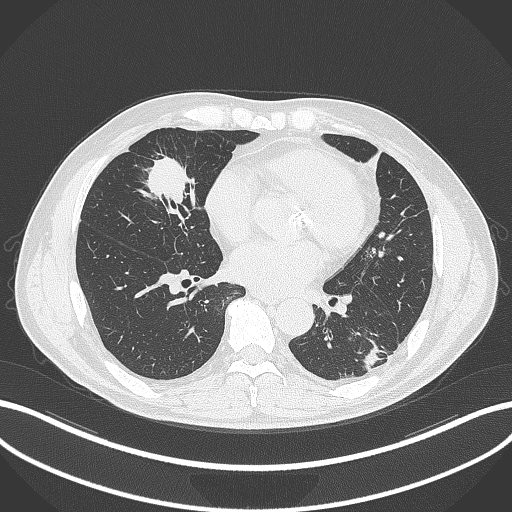
Chest CT, one axial slice; position 122 of 399 along the scan axis; lung window (W 1500 / L -600 HU); 512 × 512 image matrix, field of view 400 × 400 mm. Patient: male, 59 years. Case-level facts recorded for this patient, not image findings: clinical TNM (as recorded): T2a N1 M0.
Outlined on this slice (rectangle marked by the reading radiologist):
- lung tumour (recorded histology: adenocarcinoma): box from (x=136, y=147) to (x=200, y=211) px